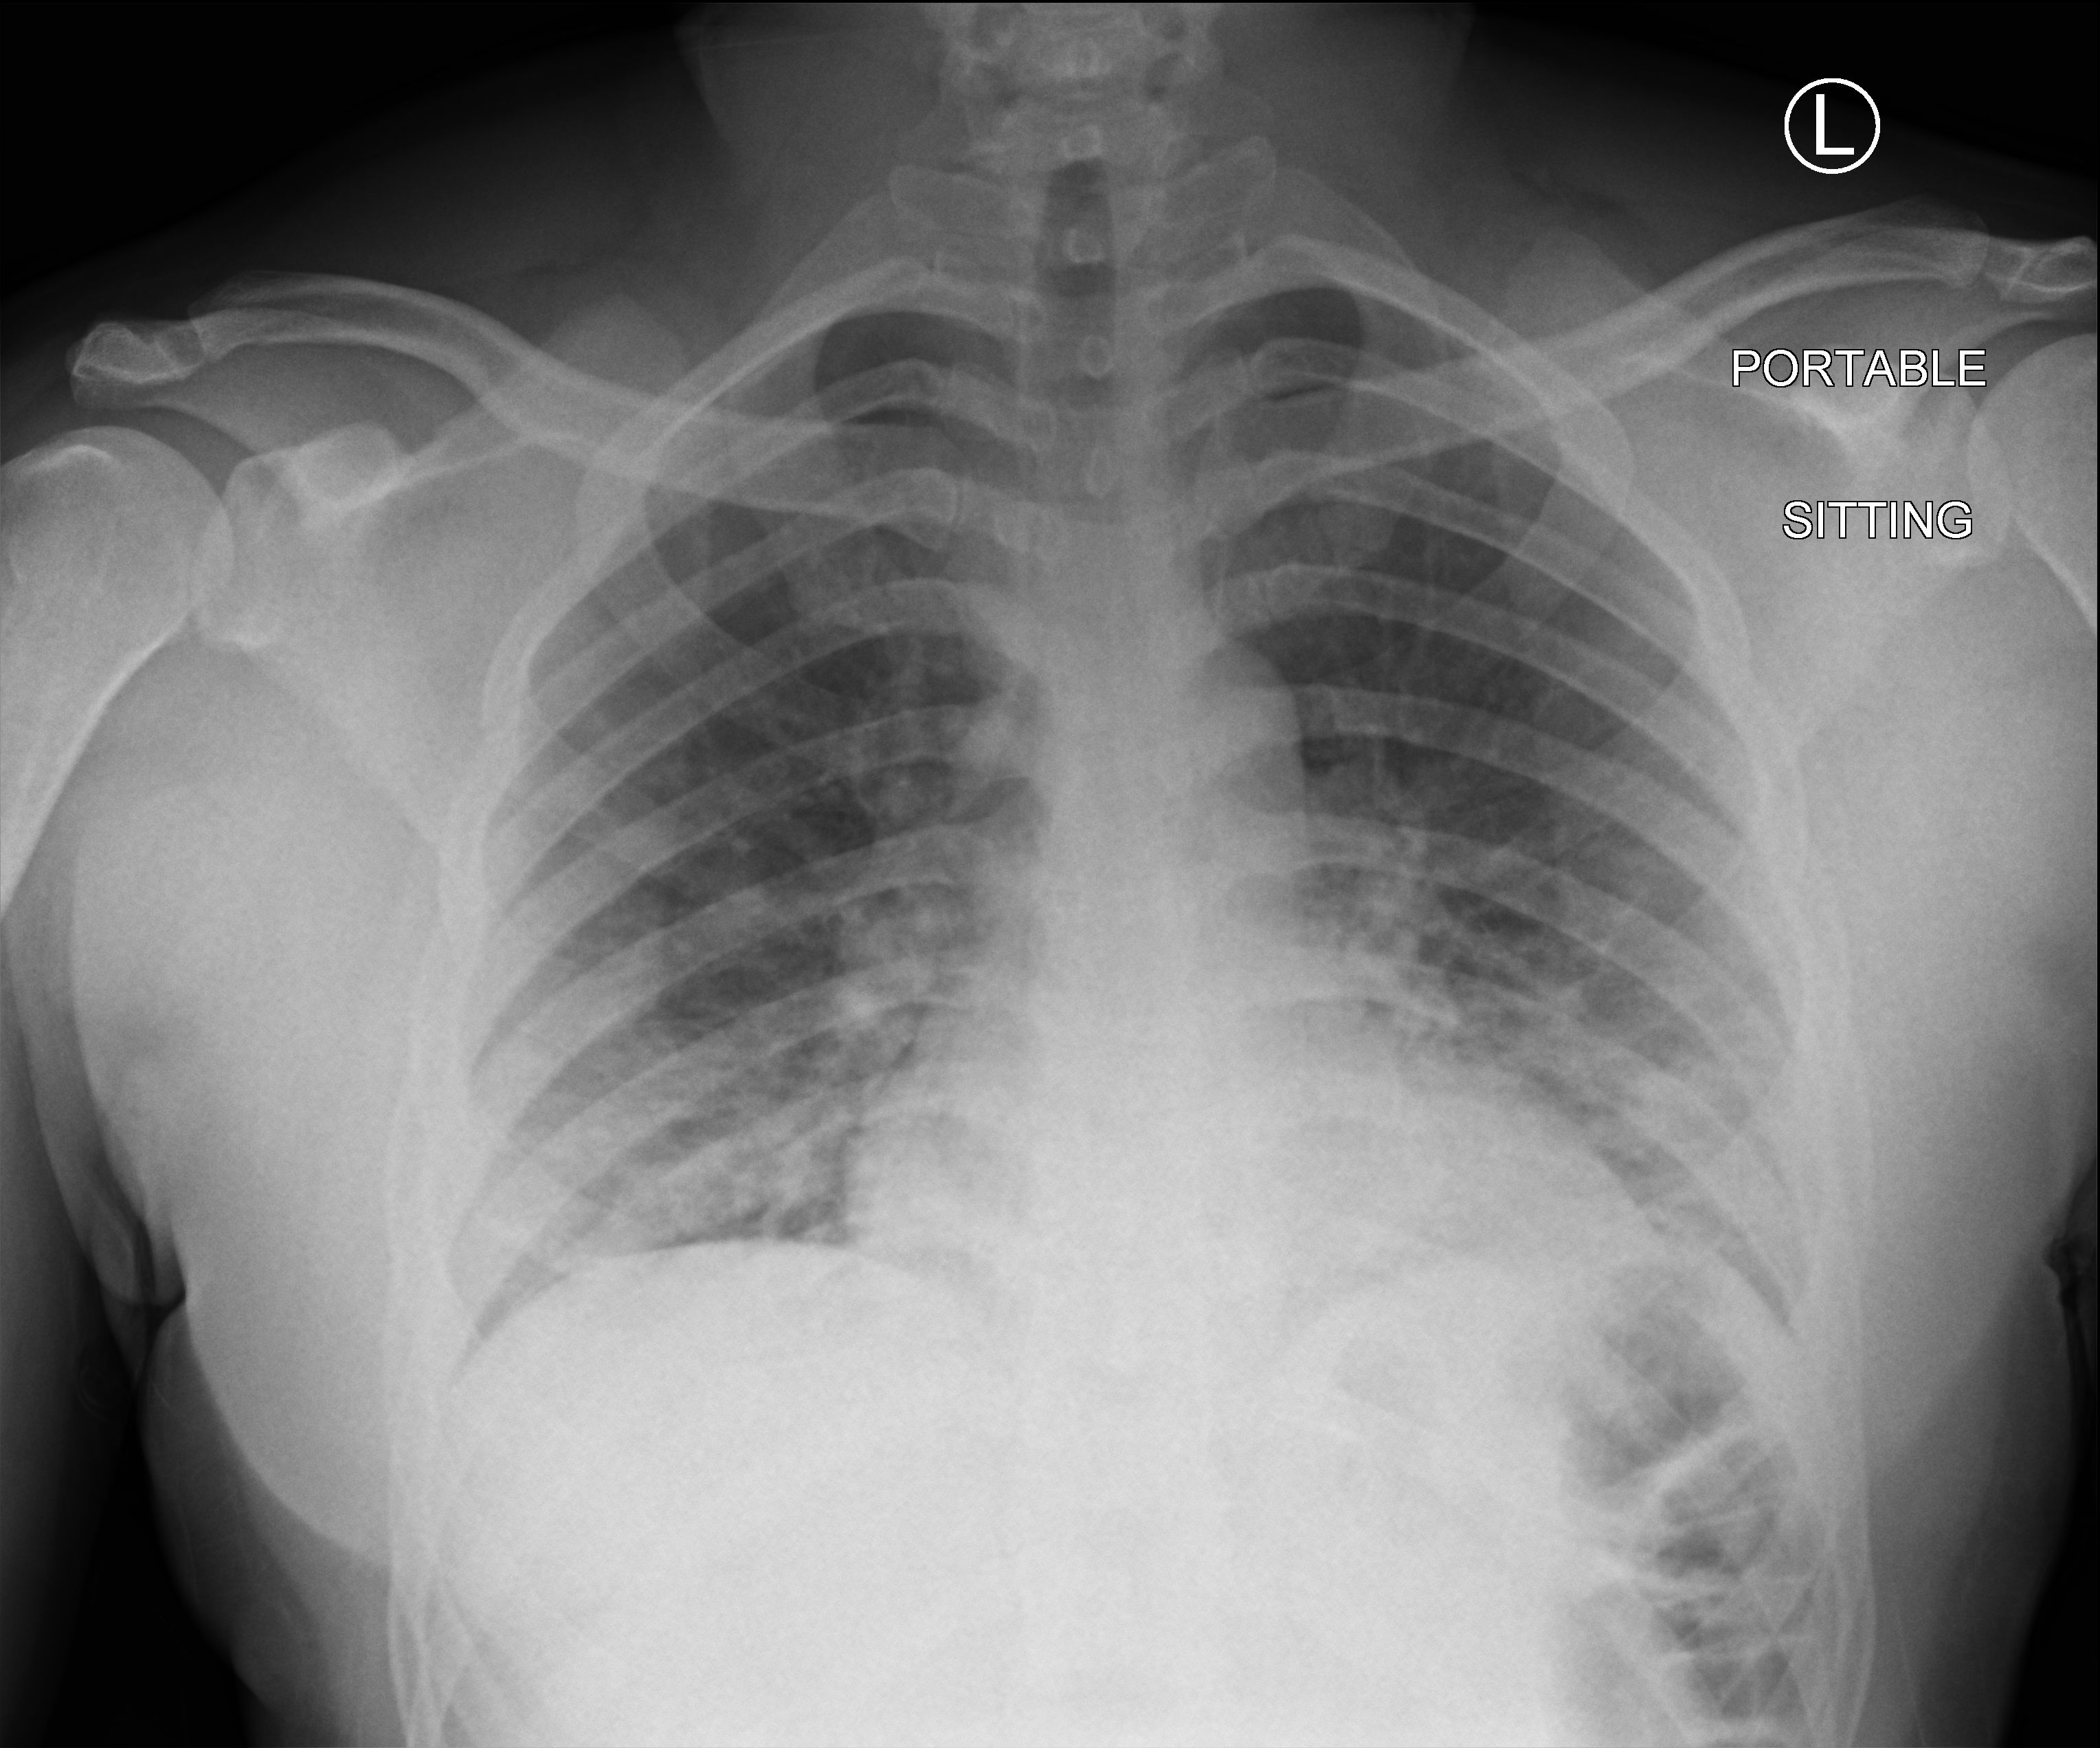
Portable chest radiograph. Male patient hospitalised with COVID-19, age 18–59 years.
Admission-level facts for this patient (not findings on this image; timing relative to this image not recorded): admitted to intensive care during this hospital stay: no.